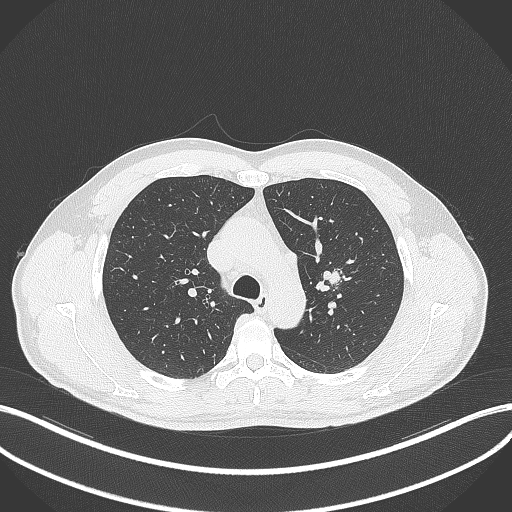
Chest CT, one axial slice; position 301 of 392 along the scan axis; reconstruction kernel B70f; 120 kVp; lung window (W 1500 / L -600 HU); 512 × 512 image matrix, field of view 400 × 400 mm. Patient: male, 50 years. From the clinical record (not read from this slice): clinical TNM (as recorded): T1c N1 M1b.
Annotated regions visible in this slice (rectangle marked by the reading radiologist):
- lung tumour (recorded histology: squamous cell carcinoma): bounding box [x1, y1, x2, y2] px = [314, 271, 340, 294]